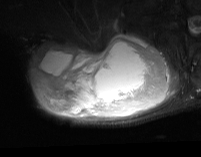
MRI of an extremity soft-tissue mass, one axial slice. Slice 44 of 74 in the series (ordered by position). STIR. MR volume resampled by the dataset authors to the PET/CT grid (not the native acquisition matrix). 3.27 mm slice thickness. 201 × 157 image matrix. Male patient. From the clinical record (not read from this slice): histological type: pleiomorphic spindle cell undifferentiated; grade: high; site of the primary tumour: right parascapusular.
Structures marked on this image (expert contour drawn on MRI and transferred to this co-registered scan by the dataset authors):
- gross tumour volume including surrounding oedema: bounding box <30,34,180,120> (left, top, right, bottom; pixels)
- gross tumour volume (mass): <33,34,171,117>